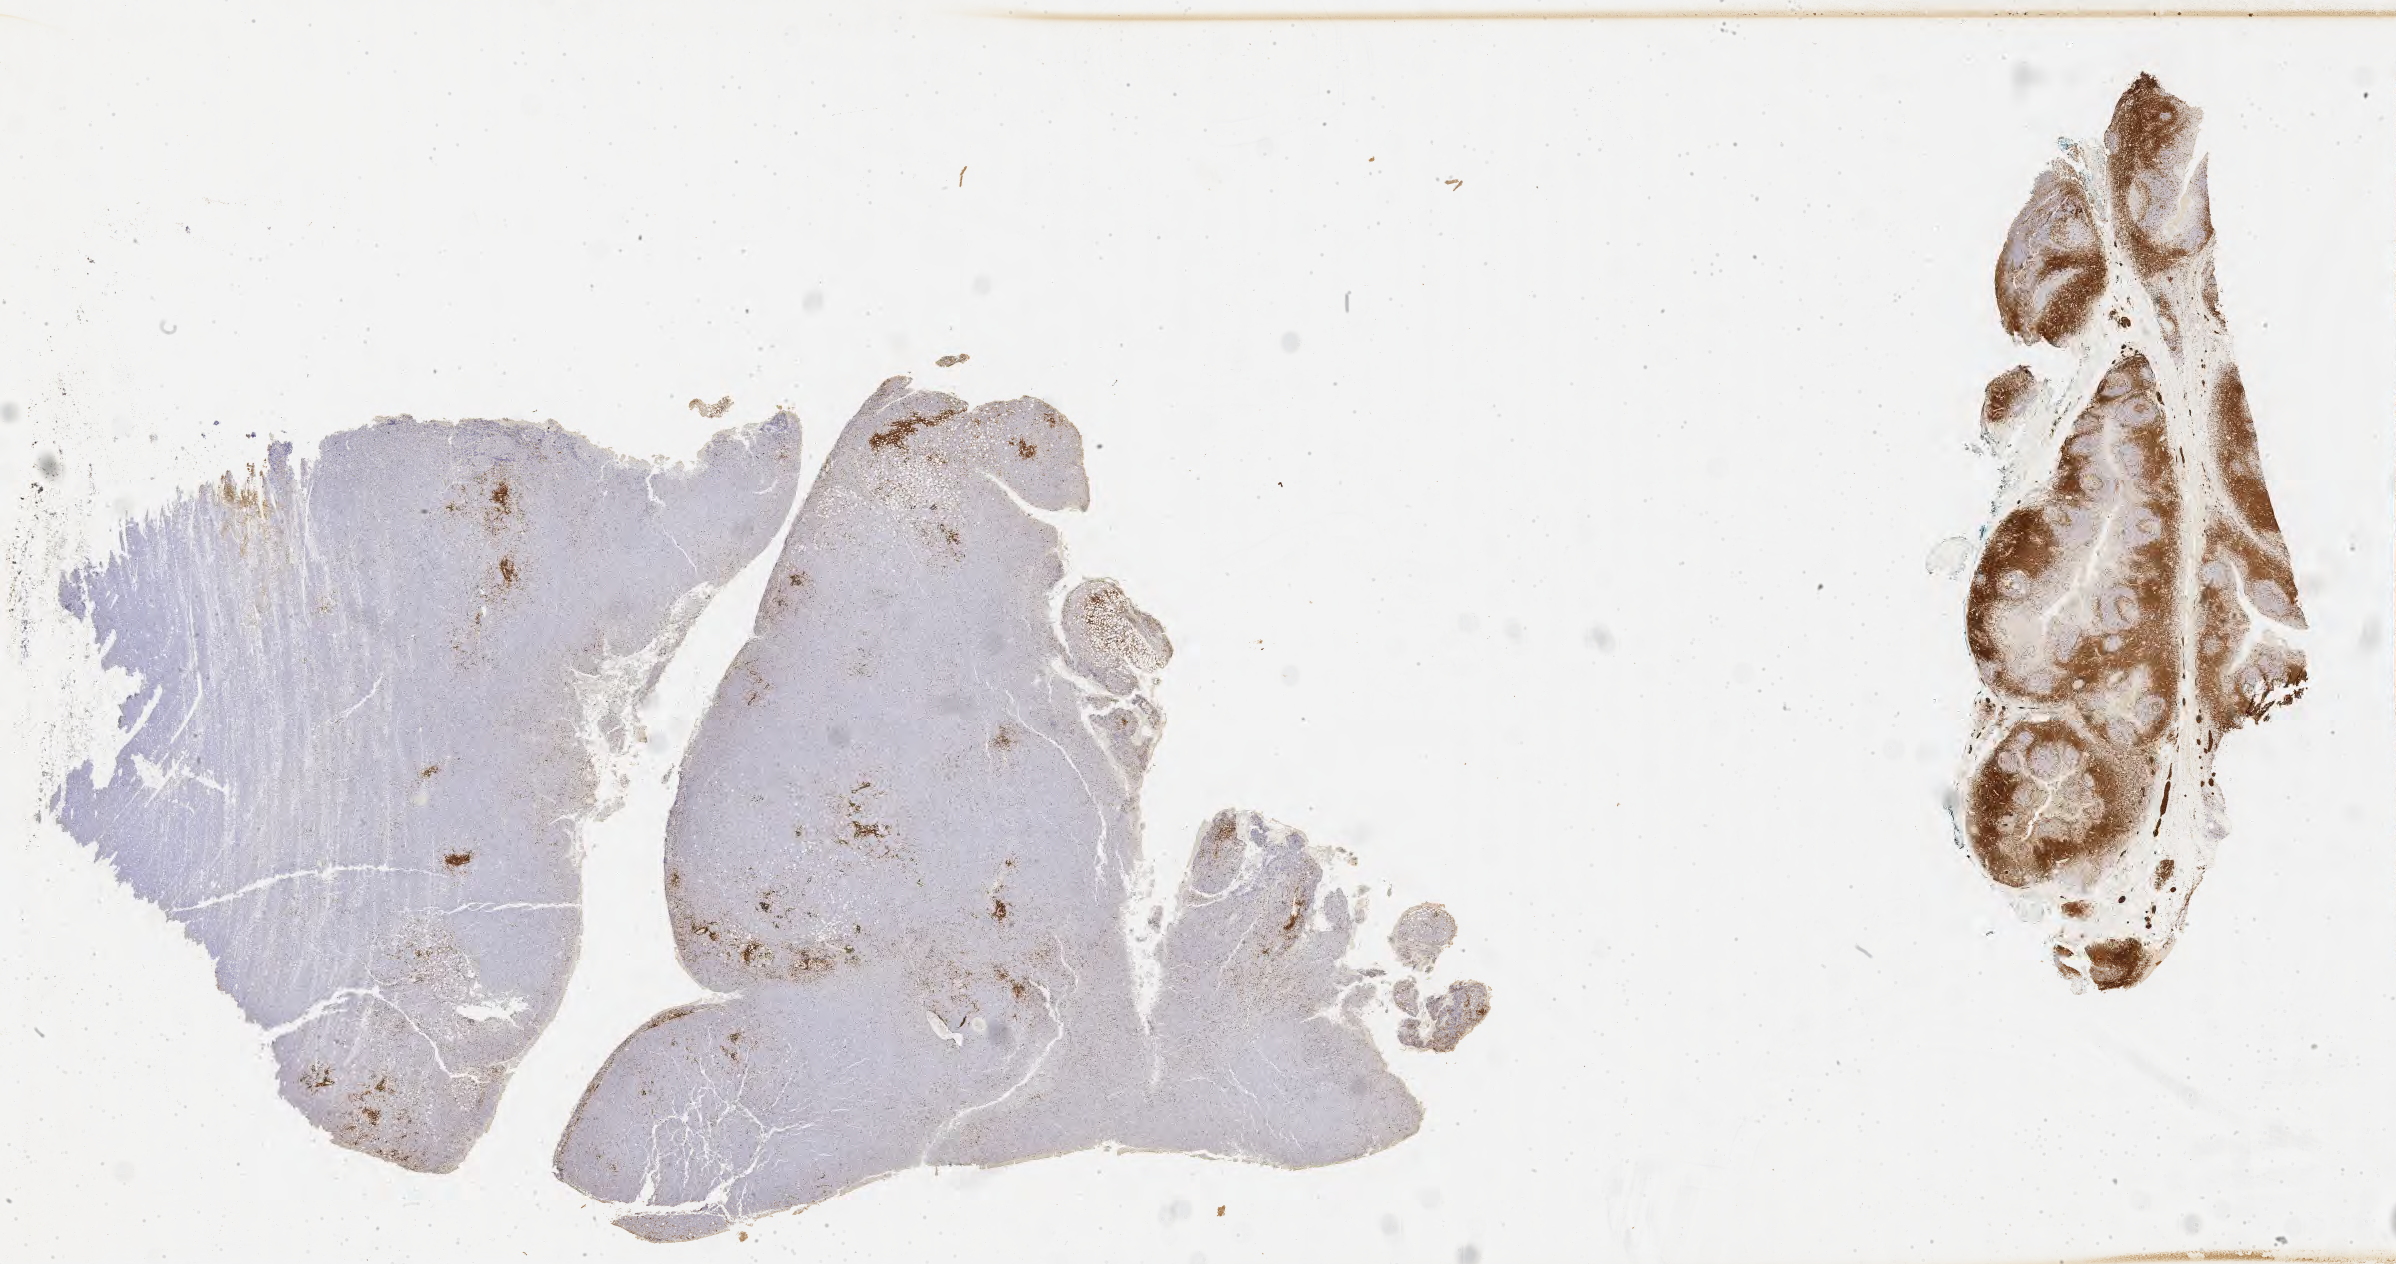
Whole-slide image, immunohistochemical stain for CD3 — low-resolution overview of the scanned area, about 38.7 x 20.4 mm; specimen: tumor tissue; anatomic site: peritoneum. Male, age 9 years at initial diagnosis.
Diagnosis: Burkitt lymphoma, NOS.